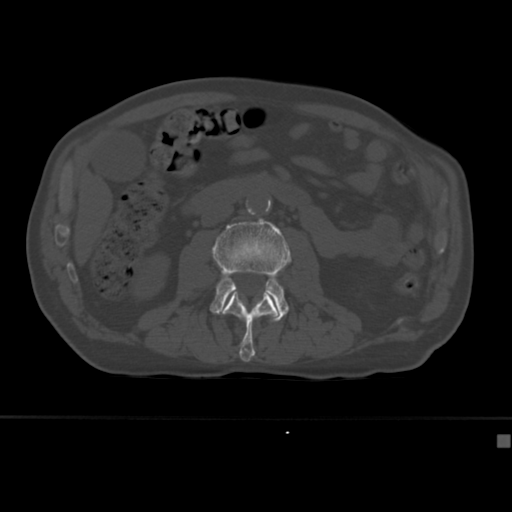
CT including the spine, one axial slice; position 137 of 430 along the scan axis; reconstruction kernel Br40s; bone window (W 1800 / L 400 HU); 512 × 512 image matrix. Male patient, age 64 years. Case-level facts recorded for this patient, not image findings: primary cancer: uterus.
Structures marked on this image (semi-automatic segmentation, software-assisted and operator-edited):
- L2 vertebra: bounding box (x1, y1, x2, y2) in pixels: (221, 292, 278, 362)
- L3 vertebra: (210, 219, 291, 322)